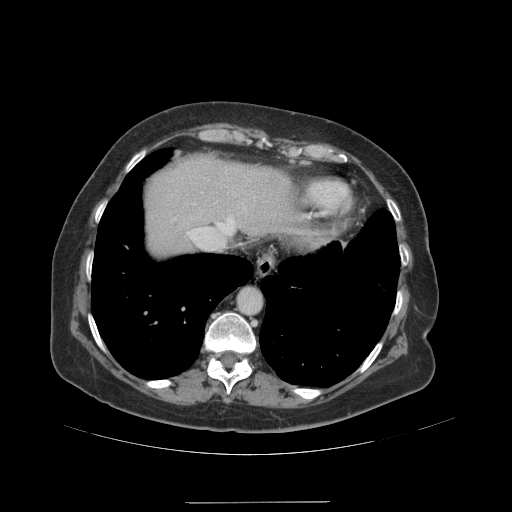
Contrast-enhanced abdominal CT (liver protocol), one axial slice. Slice 84 of 99 in the series (ordered by position). 140 kVp. Soft-tissue window (W 400 / L 40 HU). 512 × 512 image matrix. Case-level facts recorded for this patient, not image findings: diagnosis: hepatocellular carcinoma (patient treated with transarterial chemoembolisation; whether this scan precedes or follows treatment is not stated here); TNM stage (as recorded): Stage-IVA.
Annotated regions visible in this slice (semi-automatic segmentation, software-assisted and operator-edited):
- abdominal aorta: bounding box <238,288,260,314> (left, top, right, bottom; pixels)
- liver parenchyma outside the tumour (the mass and vessels are separate outlines, so this box may not span the whole liver): <146,154,289,254>
- liver vessels: <187,208,245,248>